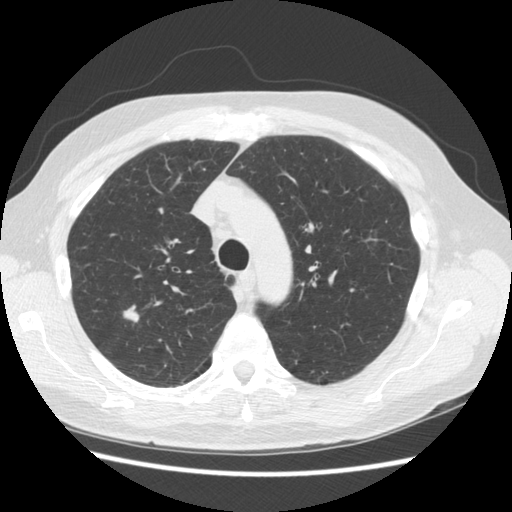
Low-dose screening chest CT, axial slice. Third screening round (two years after baseline). Lung window (W 1500 / L -600 HU). 2.5 mm slice thickness. Slice 115 of 156 in the series. Male, age 68 years at enrolment. Current smoker at enrolment.
Expert-annotated lung lesion, bounding box <105,298,153,339> (left, top, right, bottom; pixels). Screening reader's record for this exam (one nodule recorded; not confirmed to be the boxed lesion): non-calcified nodule or mass ≥4 mm, right upper lobe, 11 × 9 mm, smooth margins, soft tissue attenuation, pre-existing on the prior screen: yes; interval growth: yes. Later outcome: lung cancer diagnosed 246 days after this screen — adenocarcinoma, NOS, right upper lobe, moderately differentiated (G2), stage IA (AJCC 6th edition), 13 mm at pathology.